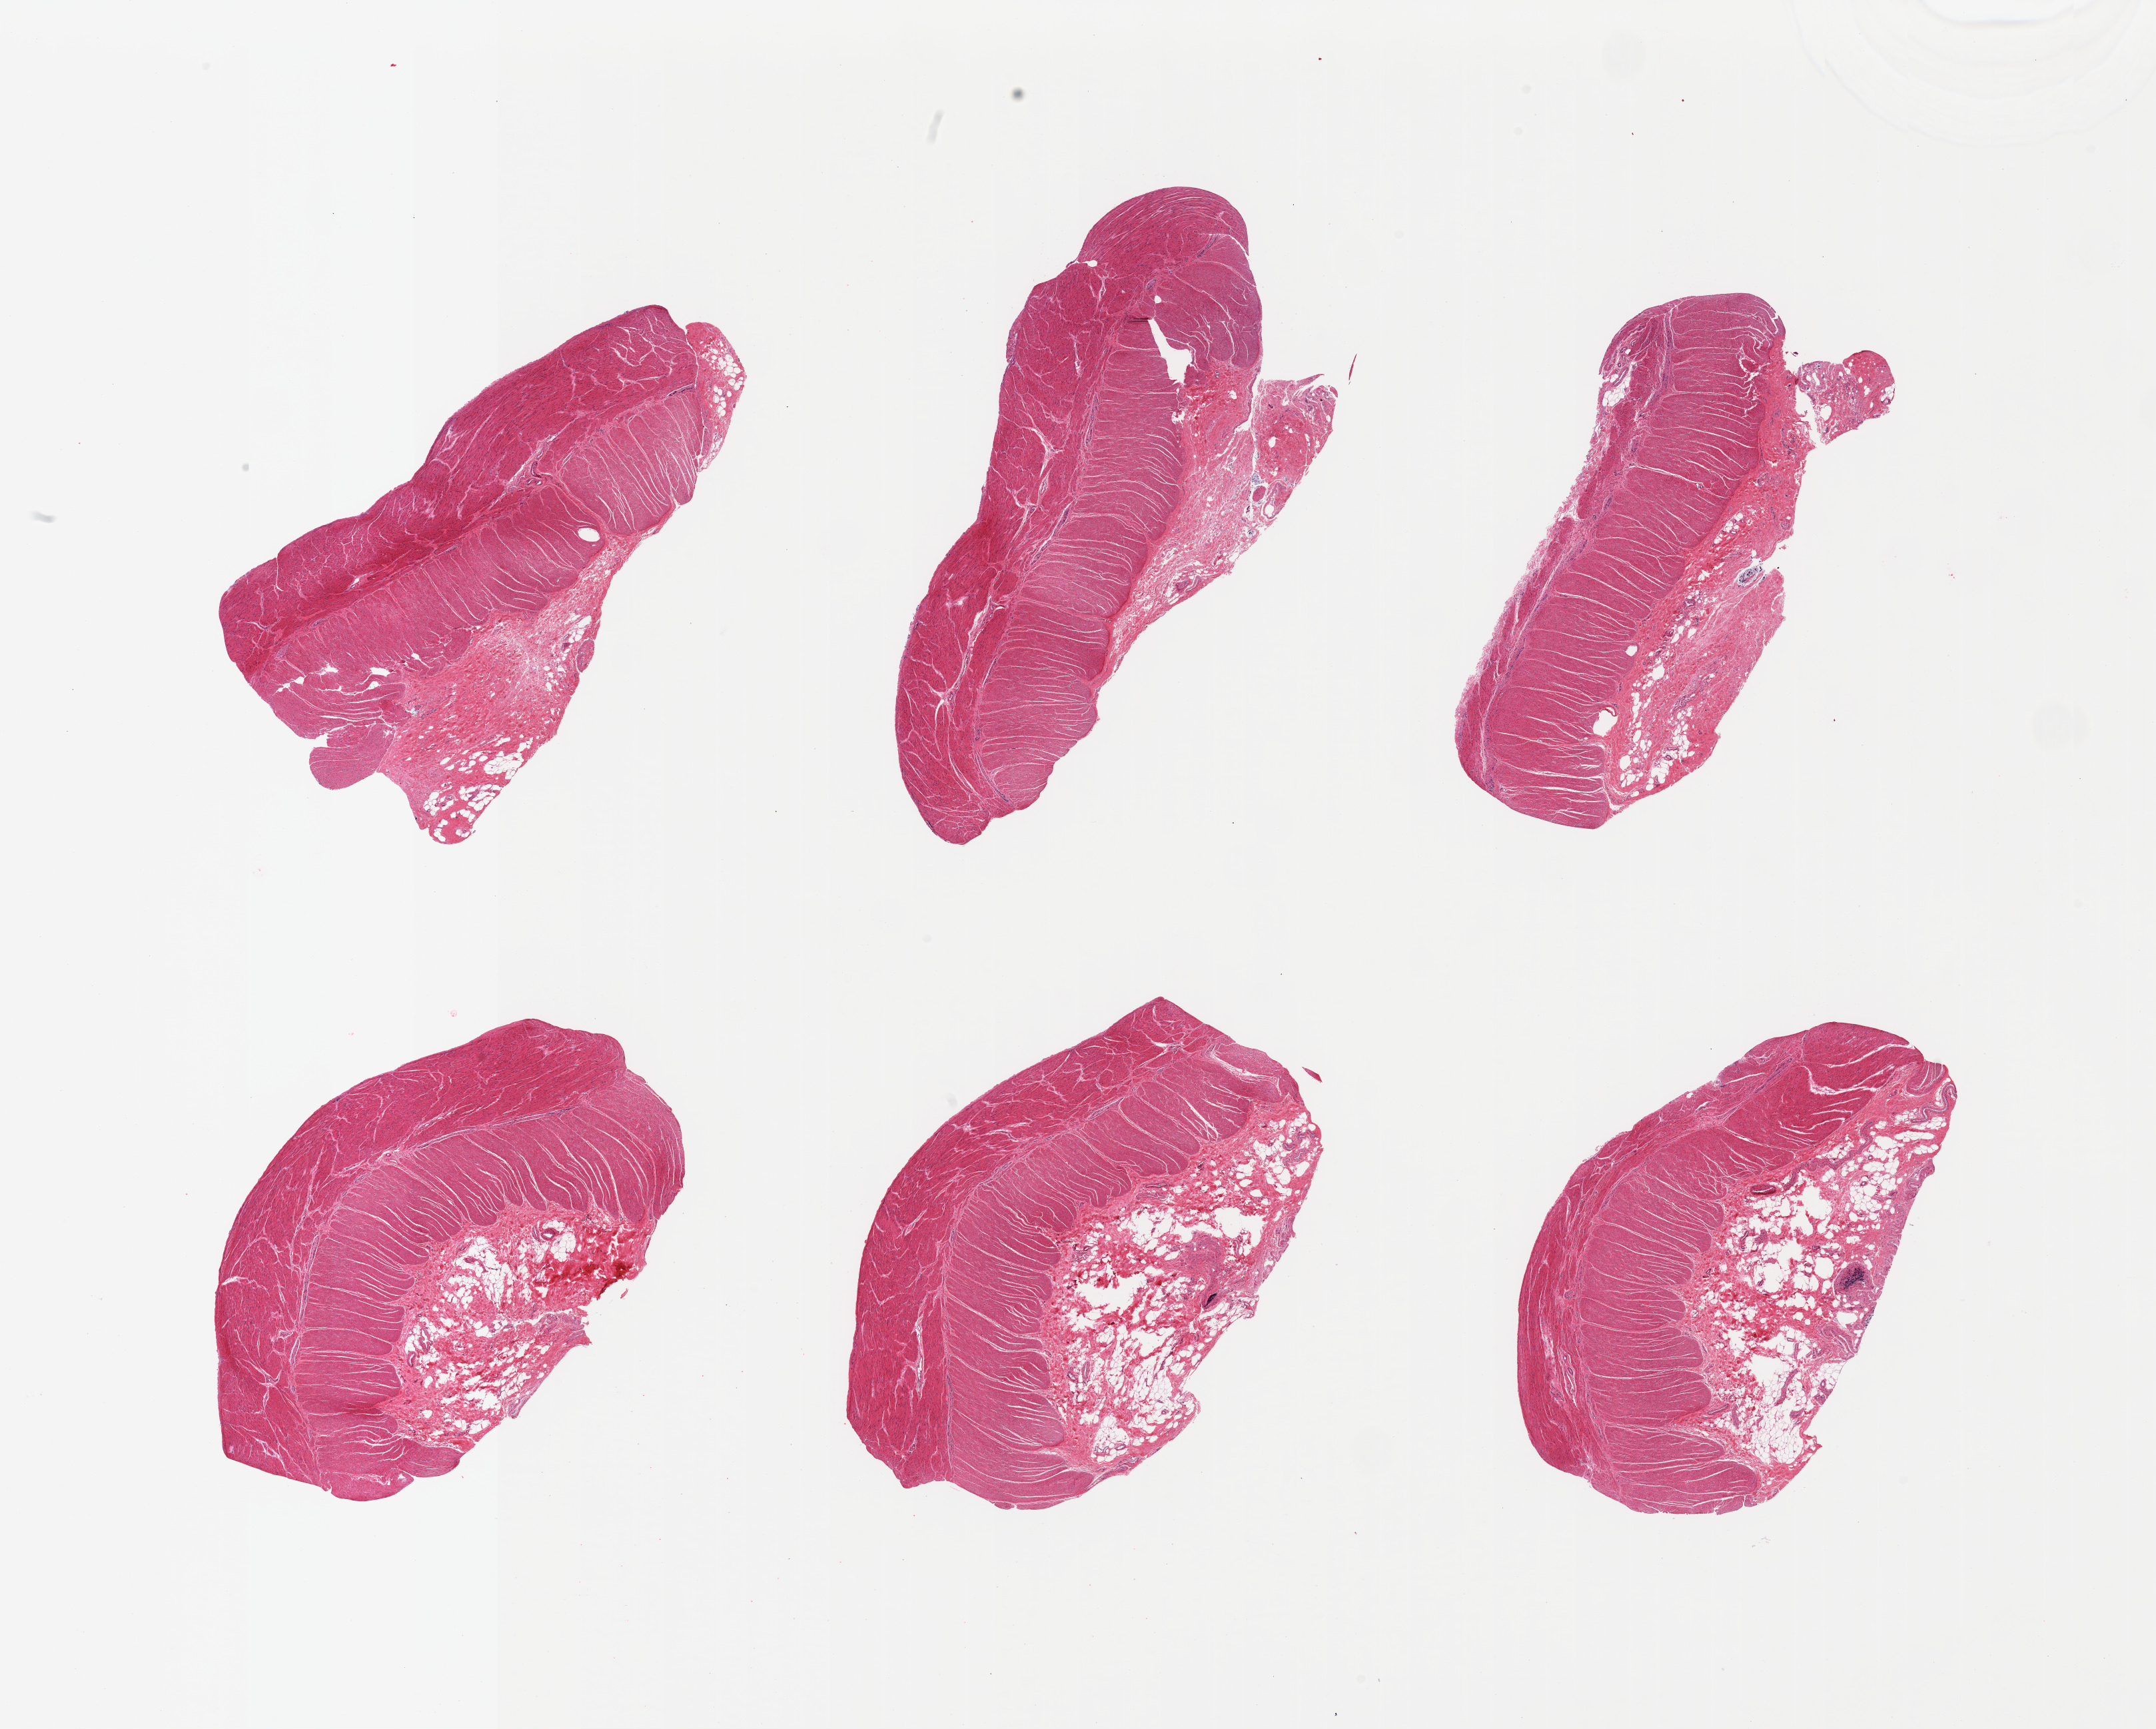
H&E whole-slide image, brightfield — low-resolution overview of the scanned area, about 25.6 x 20.5 mm (slide scanned at 20x). PAXgene-fixed paraffin-embedded (PFPE) section. Sampled site (target tissue): sigmoid colon. Donor tissue sample. Donor sex: male.
Review note (as recorded): 6 pieces, confirmed target muscularis; adherent serosal fat up to ~2mm.